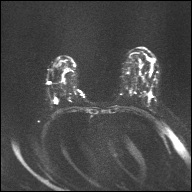
Breast MRI, one axial slice; slice 22 of 32 in the series (ordered by position); diffusion-weighted series; image 2 of 4 stored at this slice position (different b-values; order by instance number); 1.5 T; 192 × 192 image matrix, field of view 360 × 360 mm. Female patient.
Outlined on this slice (manually delineated by an expert):
- tumour on diffusion-weighted imaging: bounding box <54,97,58,102> (left, top, right, bottom; pixels)